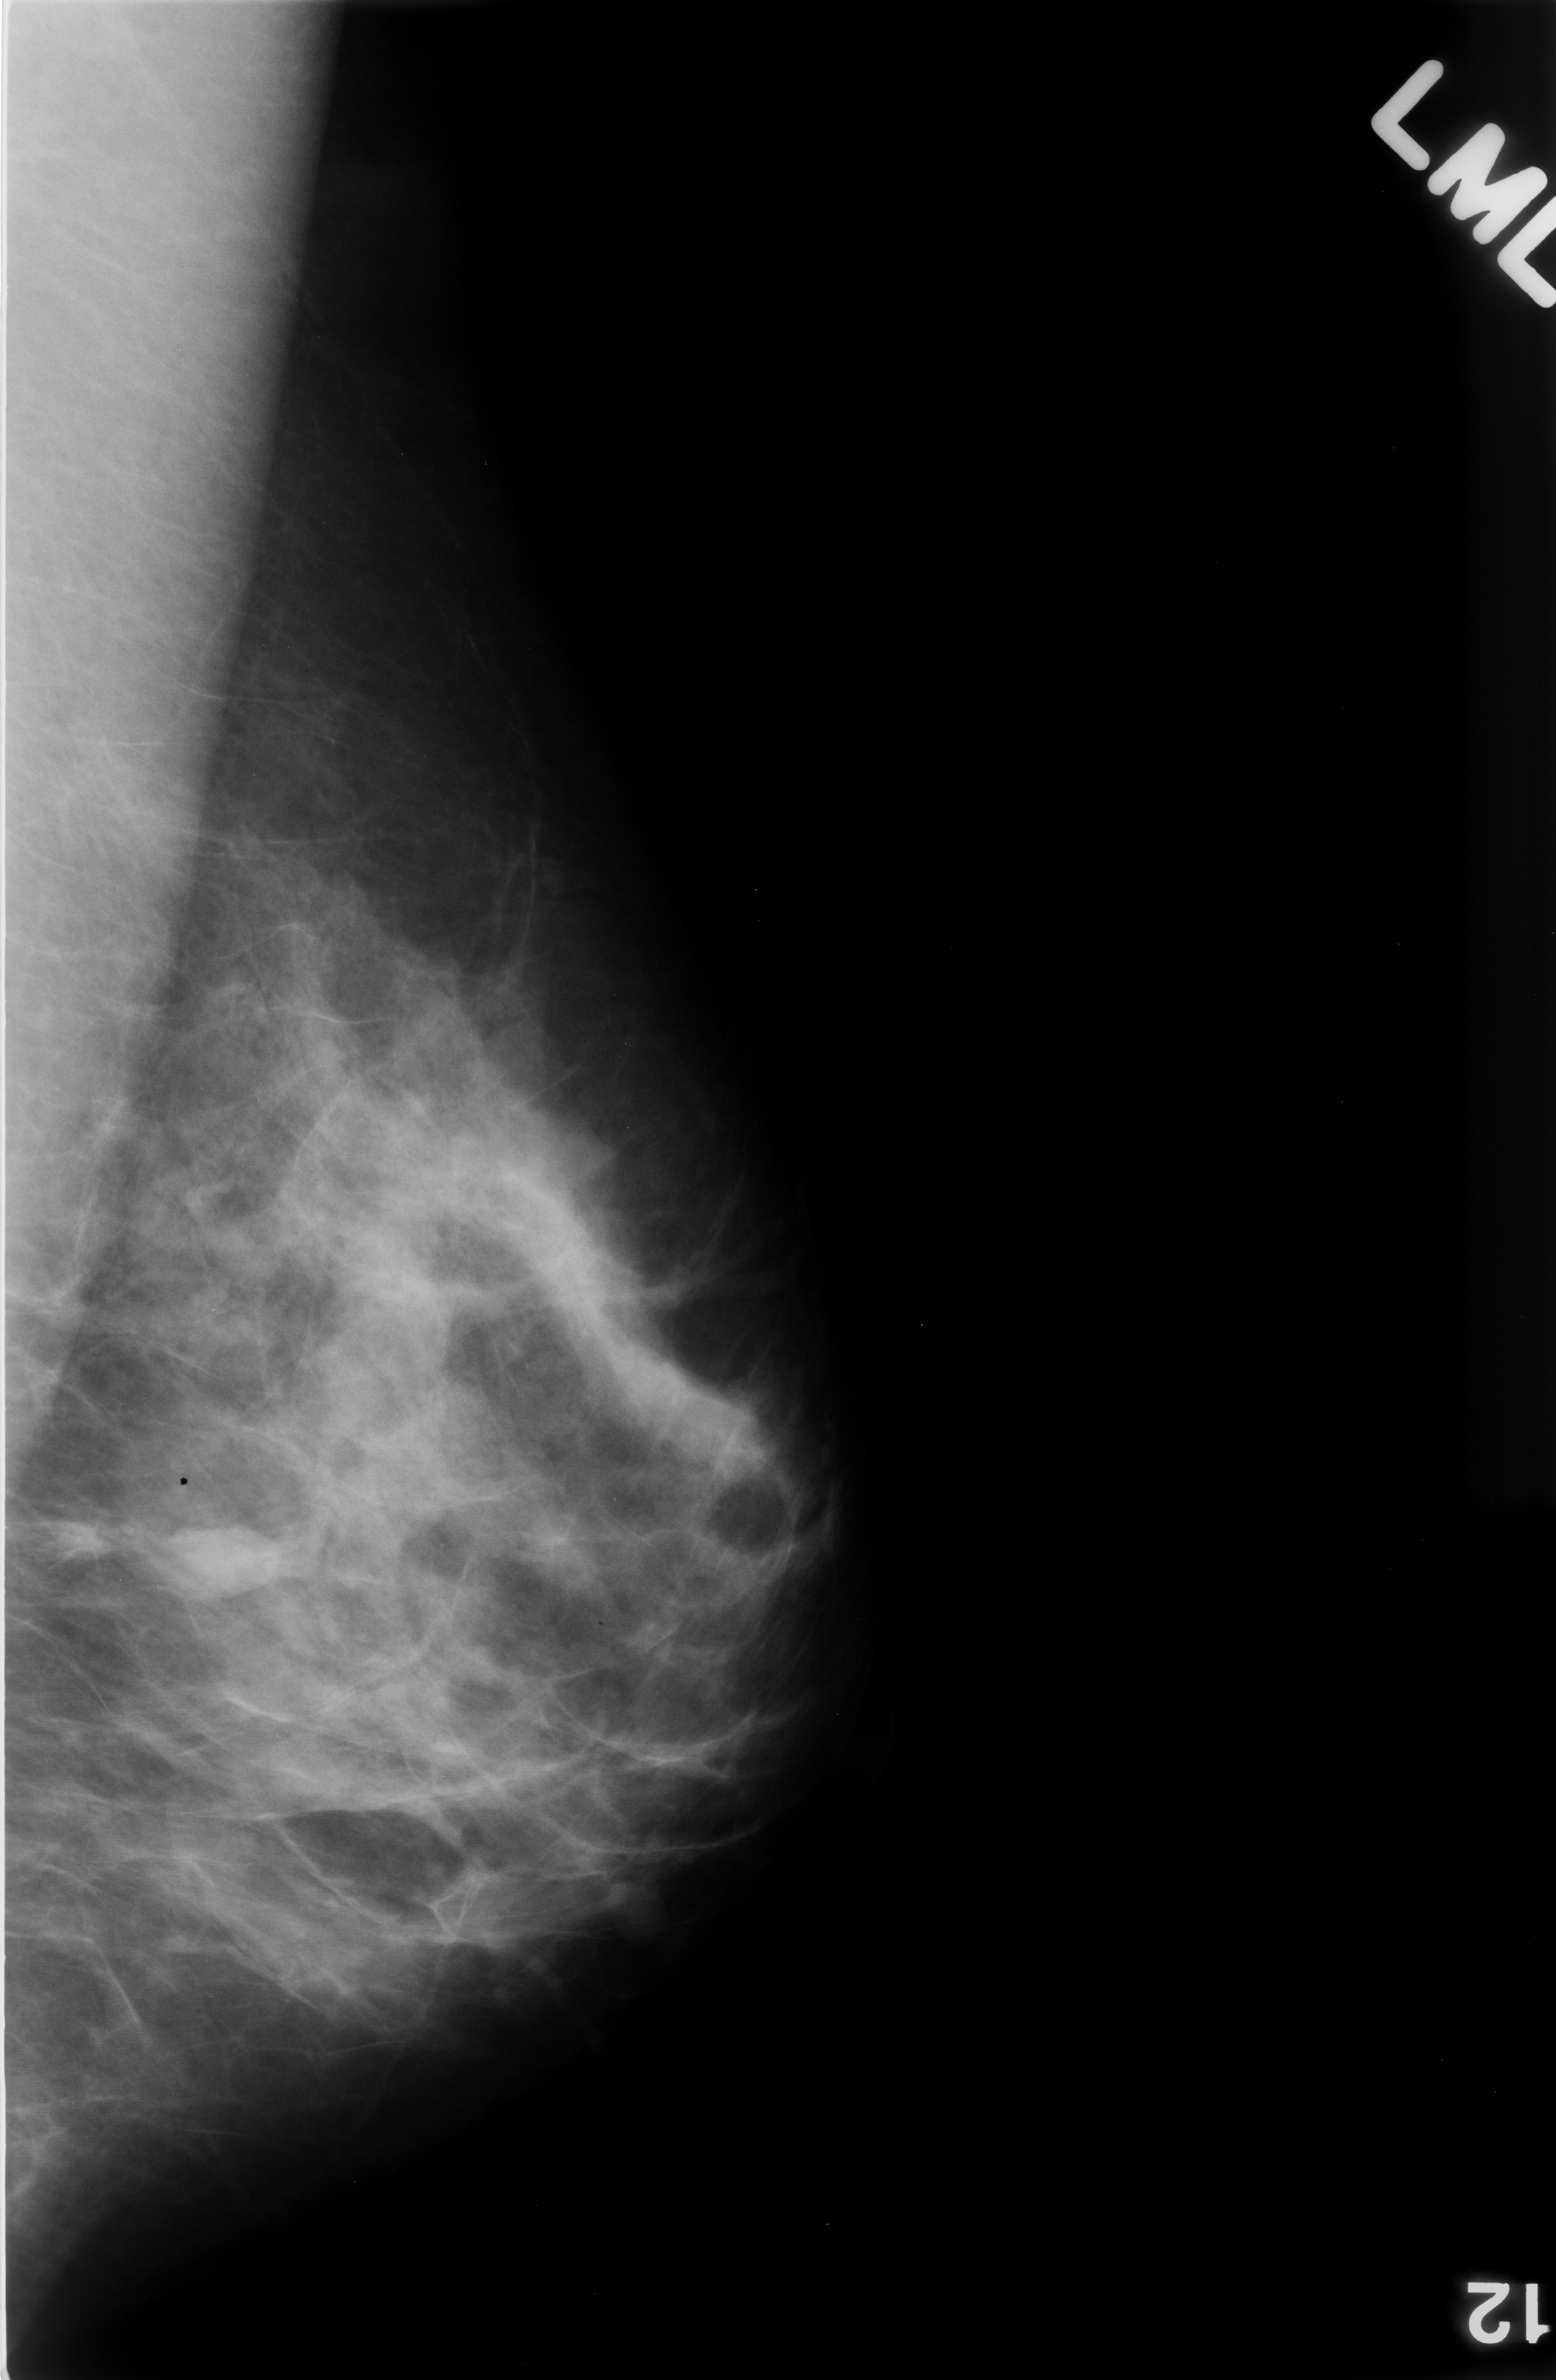
Mammogram (digitized film); left breast; mediolateral oblique (MLO) view; breast composition: scattered fibroglandular densities (BI-RADS density category 2 of 4); 1556 × 2380 image matrix.
Expert-marked regions of interest on this film, with their recorded descriptors:
- mass, shape oval, margins circumscribed; BI-RADS assessment category 3; subtlety rating 5 on a 1 (subtle) to 5 (obvious) scale; pathology (as recorded): benign: bounding box [x1, y1, x2, y2] px = [120, 1485, 285, 1606]